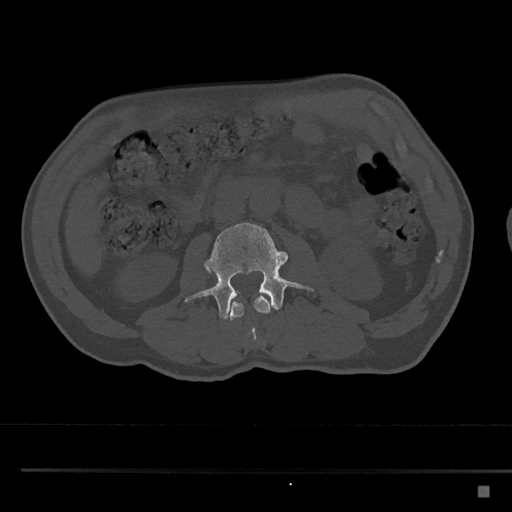
CT including the spine, one axial slice; 120 kVp; bone window (W 1800 / L 400 HU); 0.5 mm slice thickness; 512 × 512 image matrix. Male patient, age 59 years. Case-level facts recorded for this patient, not image findings: primary cancer: prostate.
Structures marked on this image (semi-automatic segmentation, software-assisted and operator-edited):
- L2 vertebra: bounding box <229,295,271,335> (left, top, right, bottom; pixels)
- L3 vertebra: <183,222,315,319>